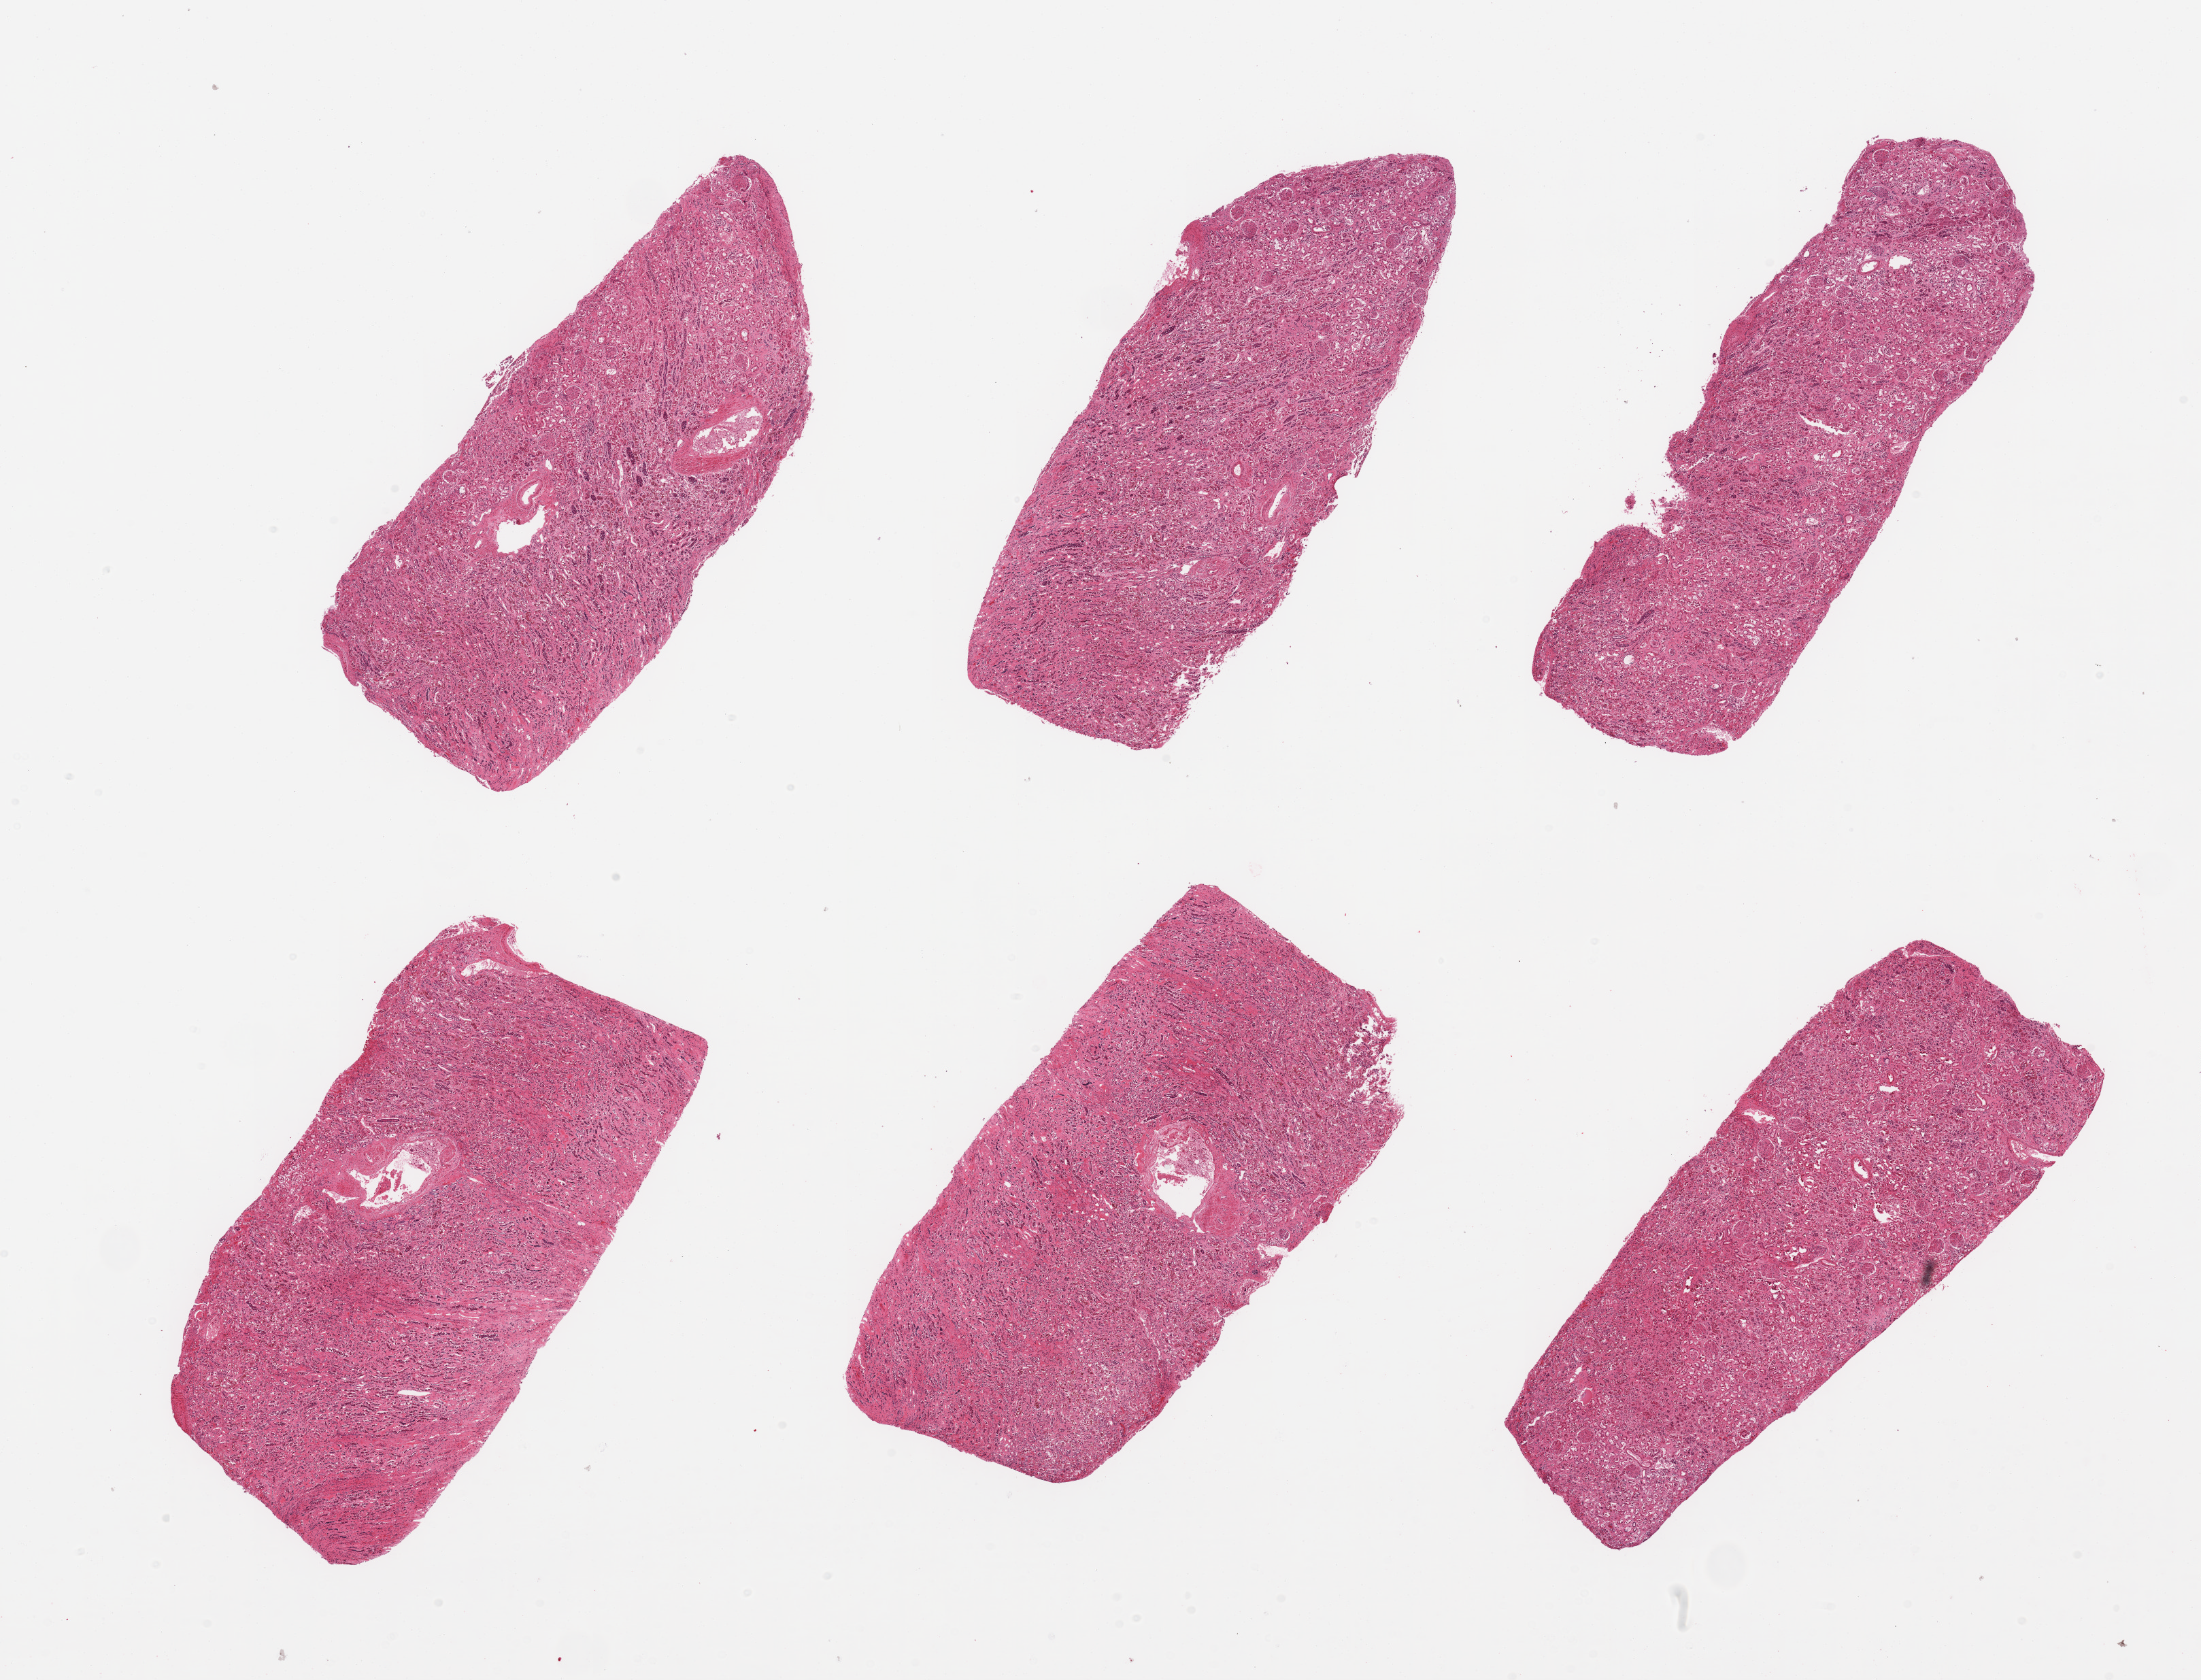
Digitized hematoxylin and eosin (H&E)-stained section, brightfield — shown as a low-resolution overview of the whole scanned area (about 25.6 x 19.5 mm); PAXgene-fixed paraffin-embedded (PFPE) section; target tissue: renal cortex; donor tissue sample. Male donor.
* reviewer comment on this tissue sample: 6 pieces; several pieces have large amounts of medulla